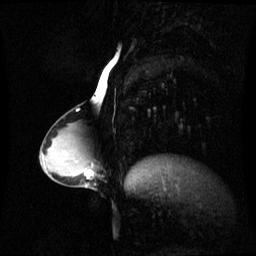
Breast MRI (dynamic contrast-enhanced), one sagittal slice. Slice 29 of 60 in the series (ordered by position). Dynamic contrast-enhanced series, image 2 of 3 at this slice position (ordered by acquisition). 1.5 T. TE 4.2 ms, TR 8.4 ms. 256 × 256 image matrix. Female patient, age 34 years. Case-level facts recorded for this patient, not image findings: setting: breast cancer imaged before/during neoadjuvant chemotherapy; receptor status: triple-negative.
Annotated regions visible in this slice (semi-automatically segmented with operator editing):
- analysis volume of interest (the breast-tissue region the enhancement analysis was run in; not a lesion): bounding box <57,156,94,189> (left, top, right, bottom; pixels)
- tumour enhancement mask (voxels above the 70 % enhancement threshold inside the analysis volume of interest): <85,170,93,177>